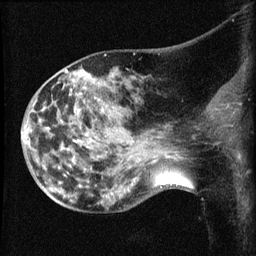
Breast MRI (dynamic contrast-enhanced), one sagittal slice; slice 27 of 60 in the series (ordered by position); dynamic contrast-enhanced series, image 2 of 3 at this slice position (ordered by acquisition); 1.5 T; TE 4.2 ms, TR 8.2 ms; 256 × 256 image matrix, field of view 180 × 180 mm. Female patient, age 50 years.
Outlined on this slice (semi-automatically segmented with operator editing):
- analysis volume of interest (the breast-tissue region the enhancement analysis was run in; not a lesion): box from (x=38, y=71) to (x=169, y=211) px
- tumour enhancement mask (voxels above the 70 % enhancement threshold inside the analysis volume of interest): (x=67, y=71)–(x=75, y=142)